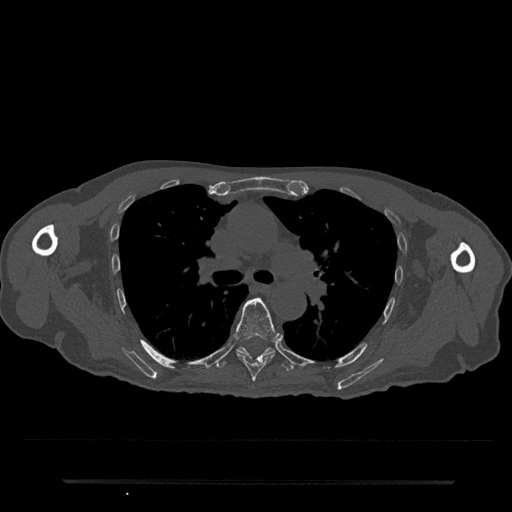
CT including the spine, one axial slice. Position 515 of 797 along the scan axis. 120 kVp. Bone window (W 1800 / L 400 HU). 512 × 512 image matrix. Patient: male, 74 years. Case-level facts recorded for this patient, not image findings: primary cancer: prostate.
Structures marked on this image (semi-automatic segmentation, software-assisted and operator-edited):
- T6 vertebra: bounding box [x1, y1, x2, y2] px = [234, 298, 279, 382]
- T7 vertebra: [216, 347, 294, 371]